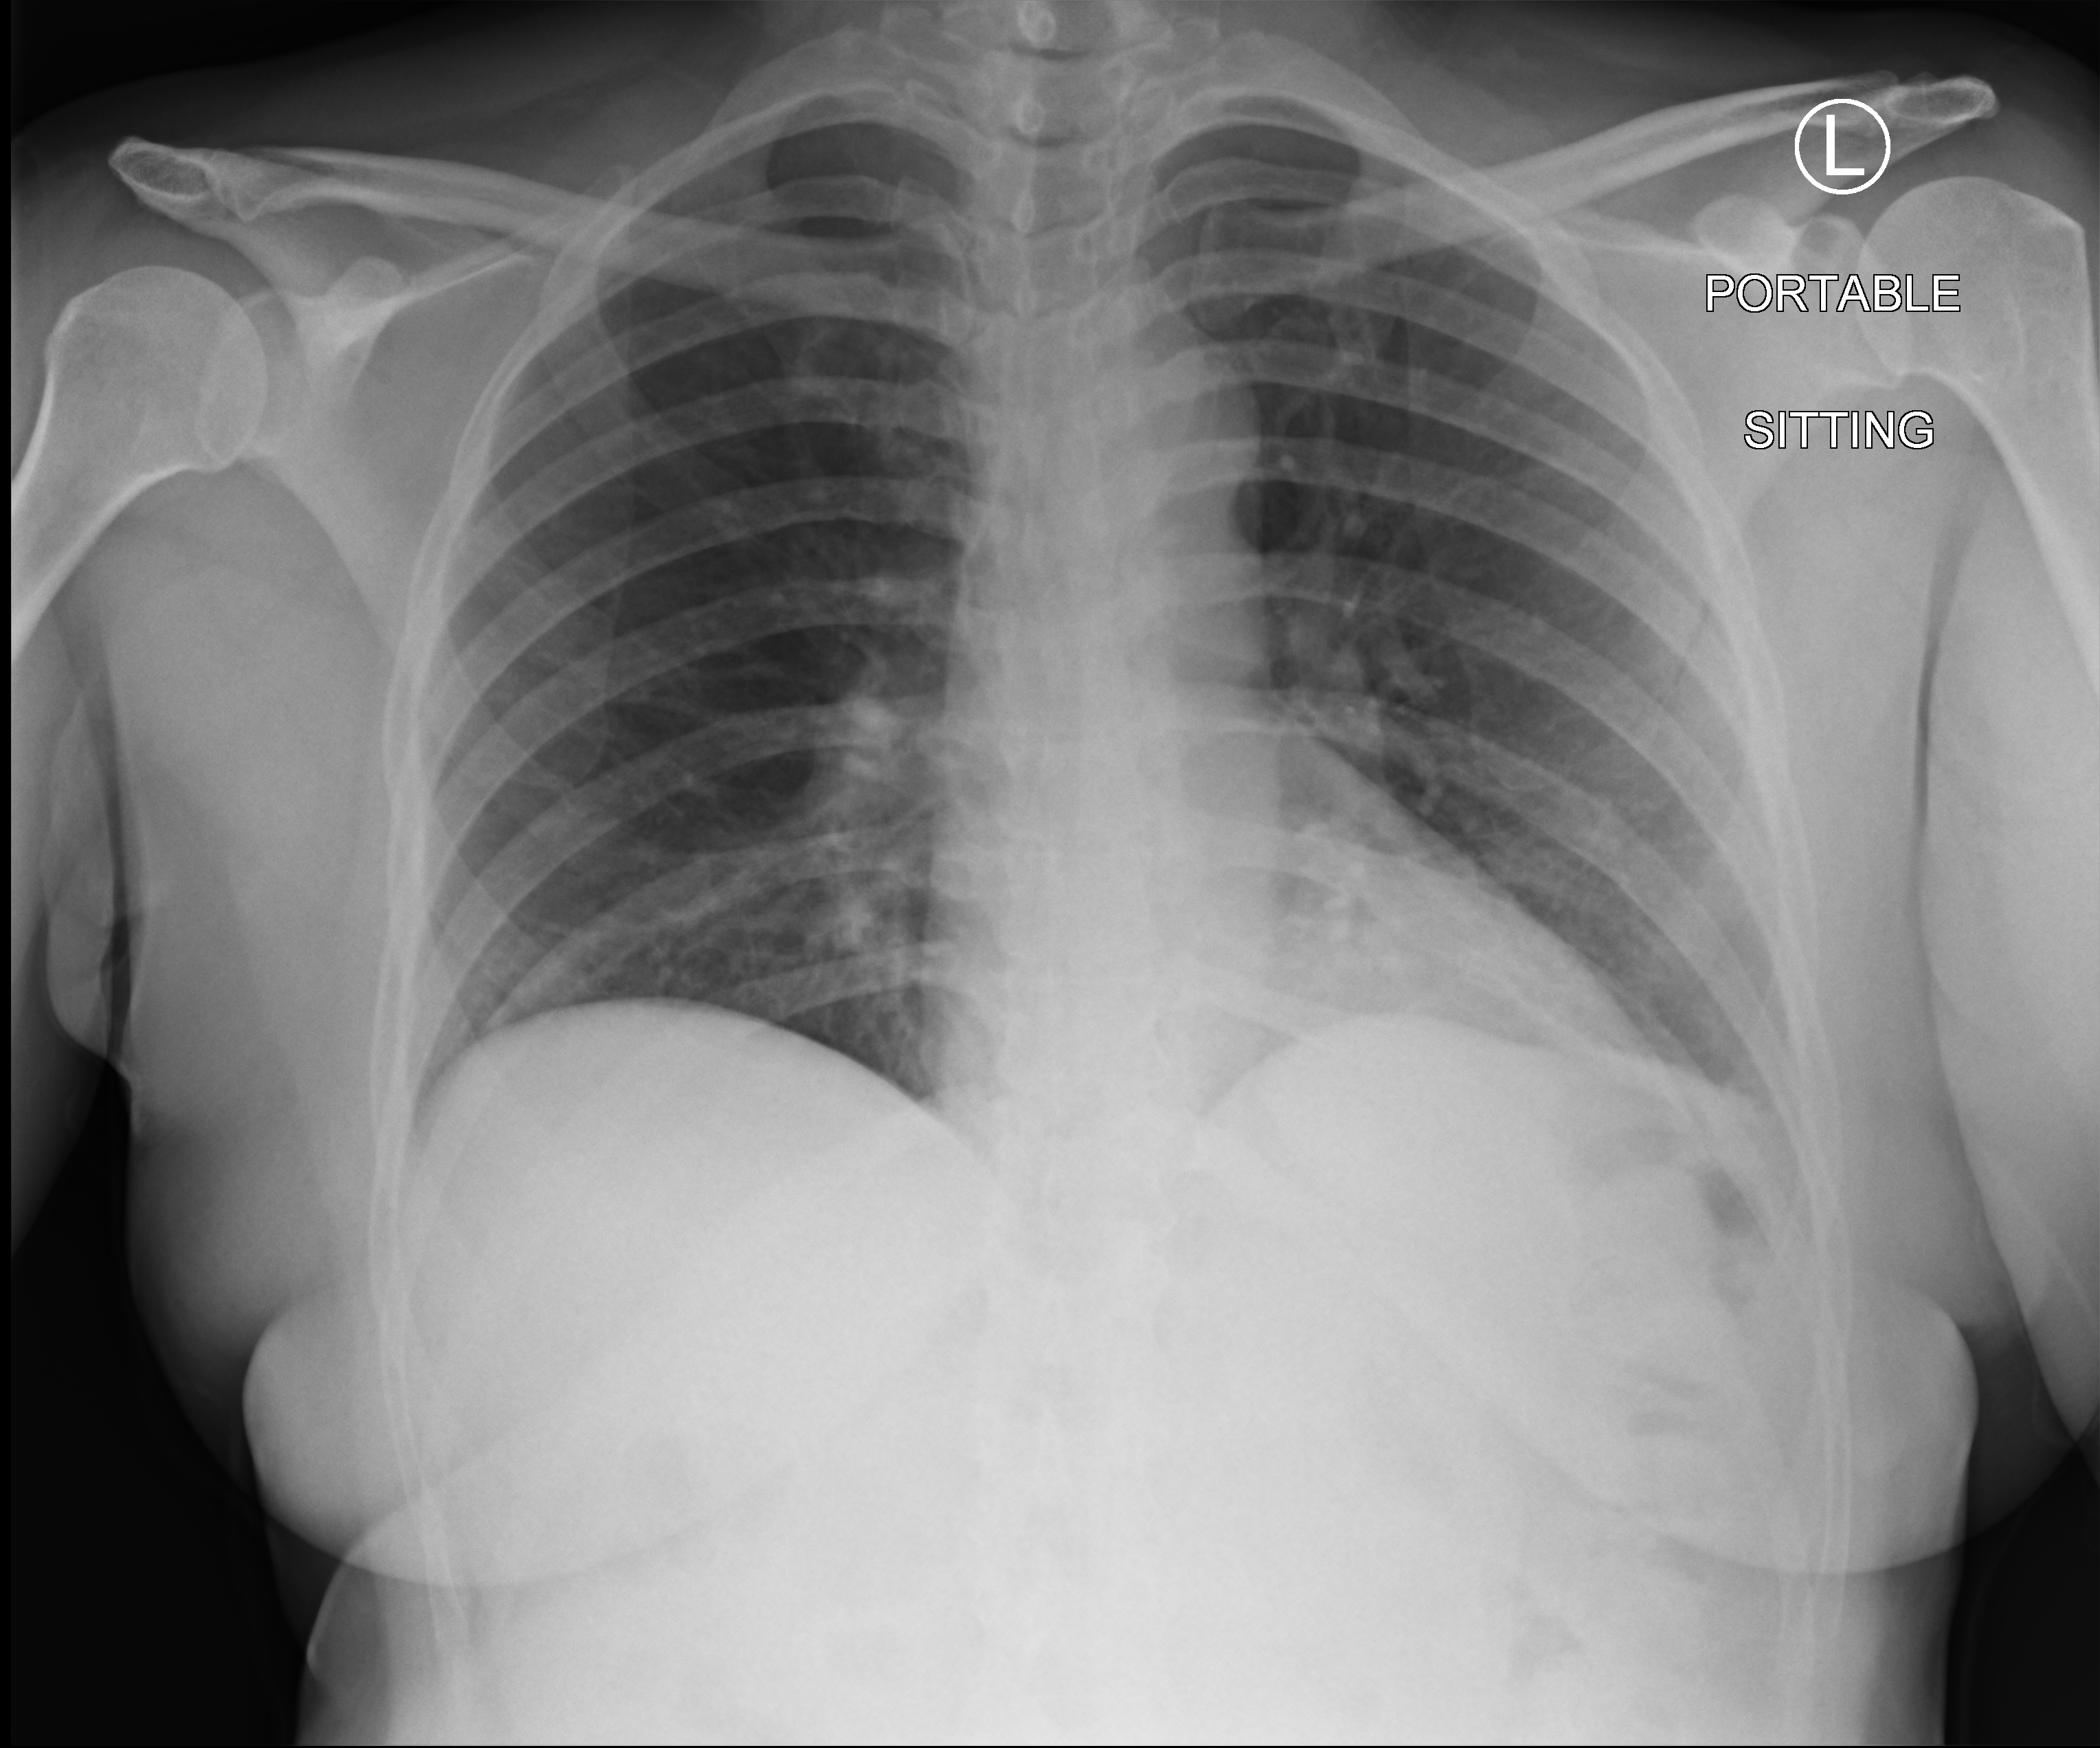
Chest X-ray (portable), anteroposterior (AP) projection. Female patient hospitalised with COVID-19, age 18–59 years.
Hospital-stay facts (about this admission, not read from this image; timing relative to this image not recorded): mechanically ventilated during this hospital stay: no; admitted to intensive care during this hospital stay: no; length of hospital stay: 1 day.